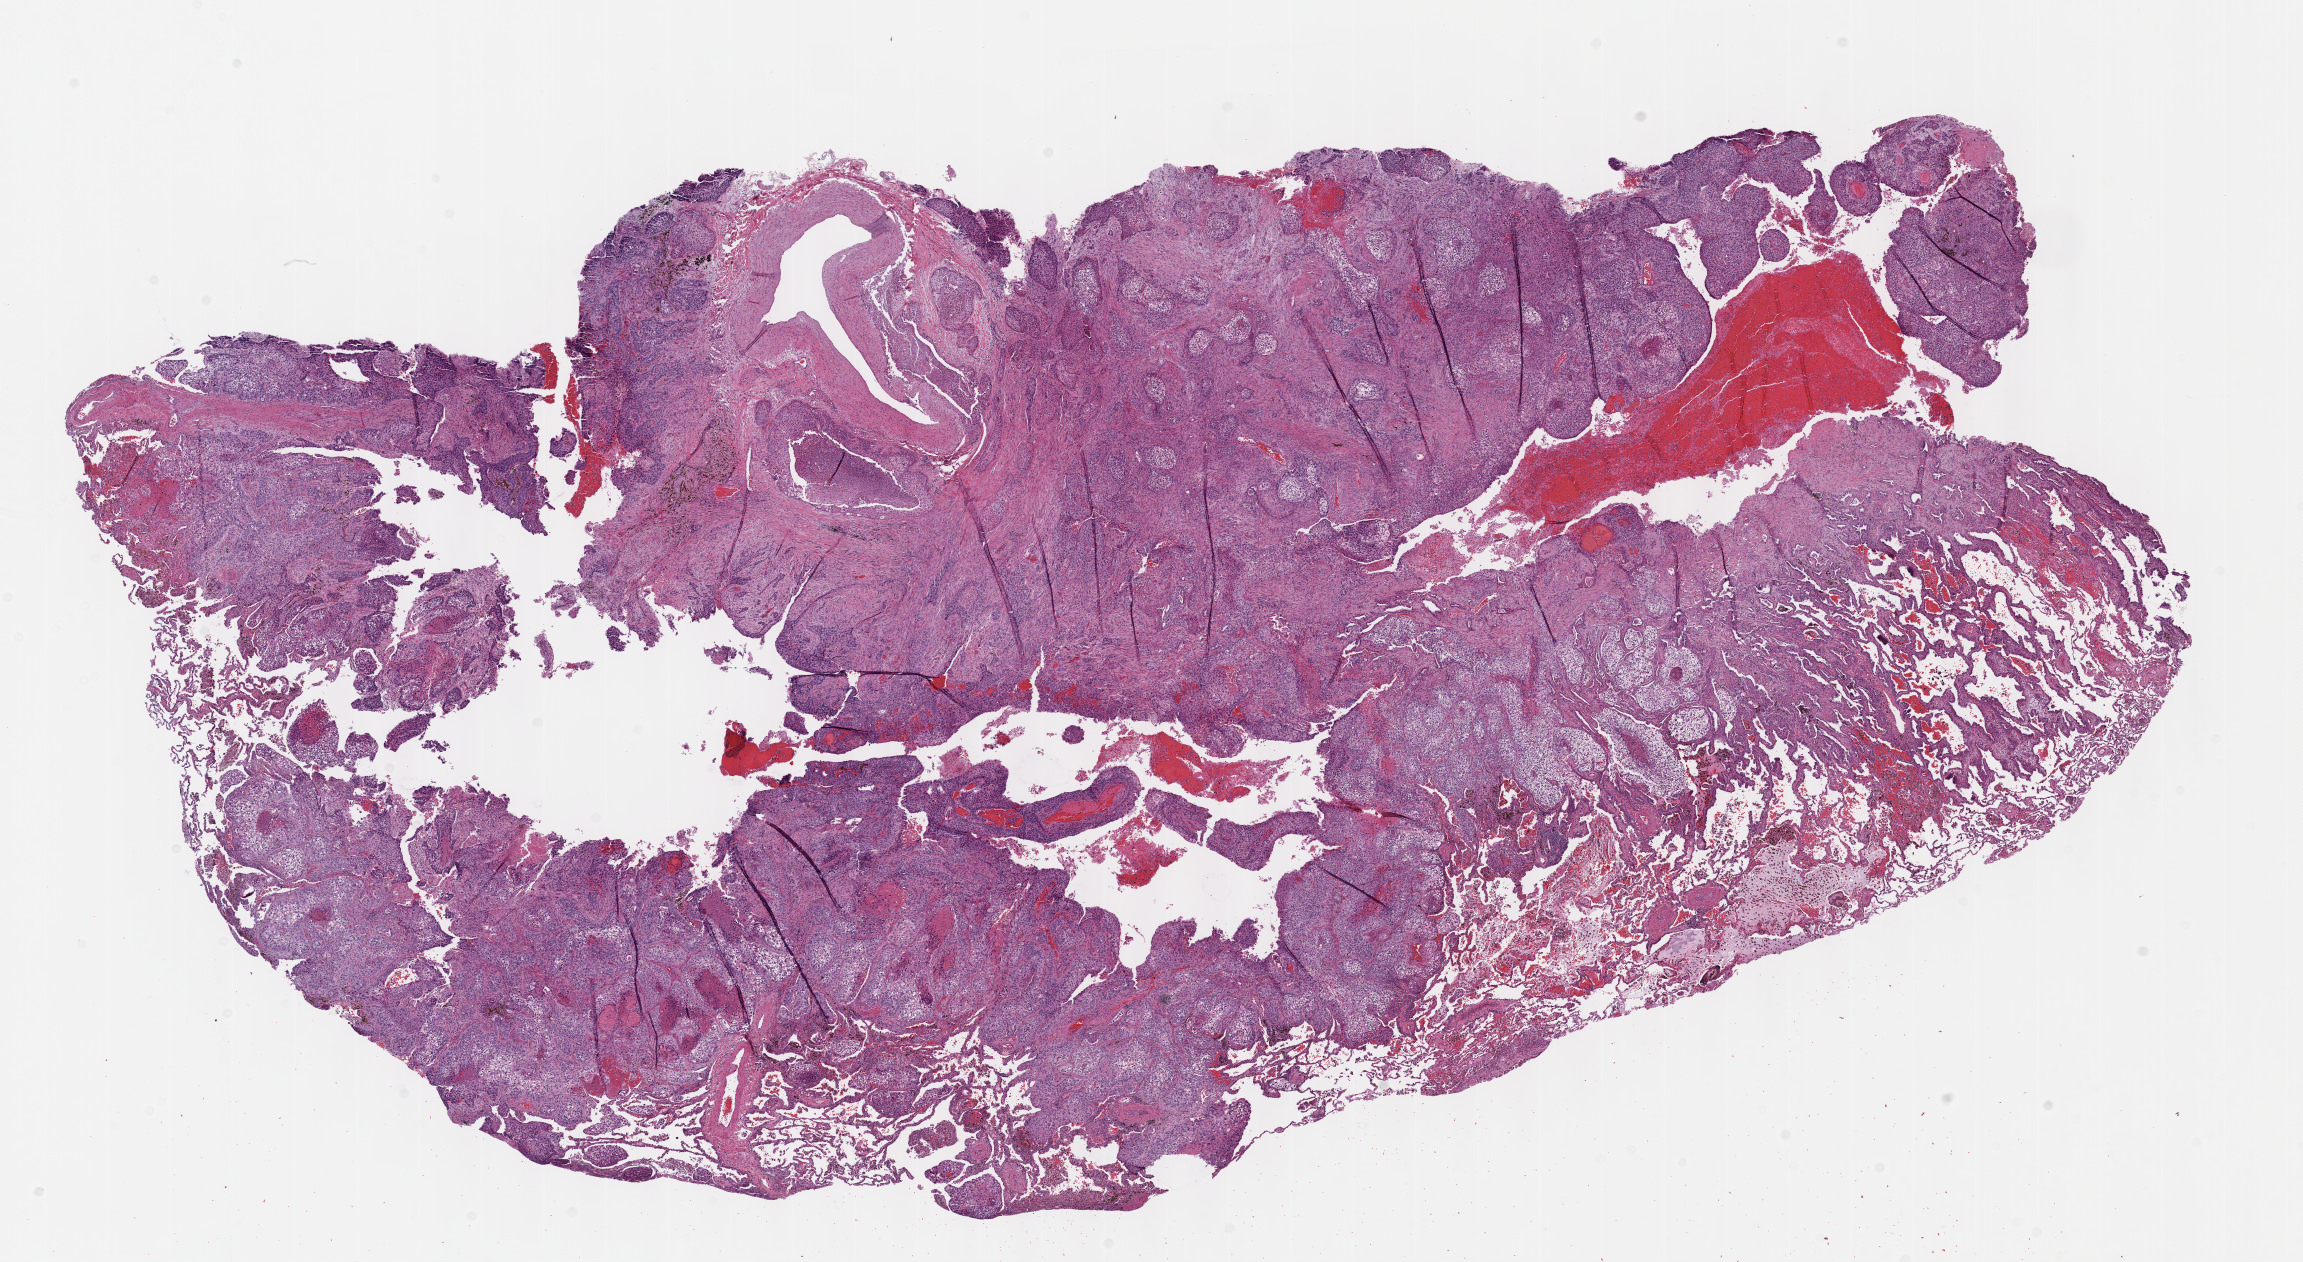
Digitized Hematoxylin and eosin (H&E) stained tissue section (whole slide) — whole scanned area (about 18.6 x 10.2 mm, acquisition: 40x scan) shown as a low-resolution overview. Formalin-fixed paraffin-embedded (FFPE) diagnostic section. Primary tumour sample from the lung. Patient: male, age at initial diagnosis 65 years.
AJCC pathologic stage: IB. Pathologic diagnosis: Squamous cell carcinoma, NOS.